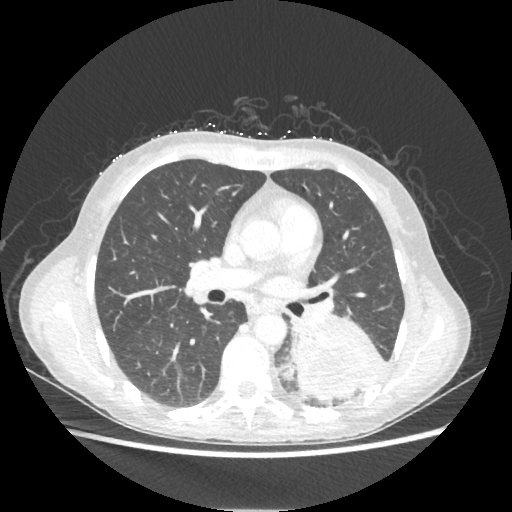
Chest CT, one axial slice. Position 122 of 221 along the scan axis. Reconstruction kernel STANDARD. 80 kVp. Lung window (W 1500 / L -600 HU). 512 × 512 image matrix, field of view 360 × 360 mm. Patient: female, 53 years. Case-level facts recorded for this patient, not image findings: clinical TNM (as recorded): T3 N0 M0.
Outlined on this slice (rectangle marked by the reading radiologist):
- lung tumour (recorded histology: adenocarcinoma): bounding box [x1, y1, x2, y2] px = [290, 317, 383, 399]